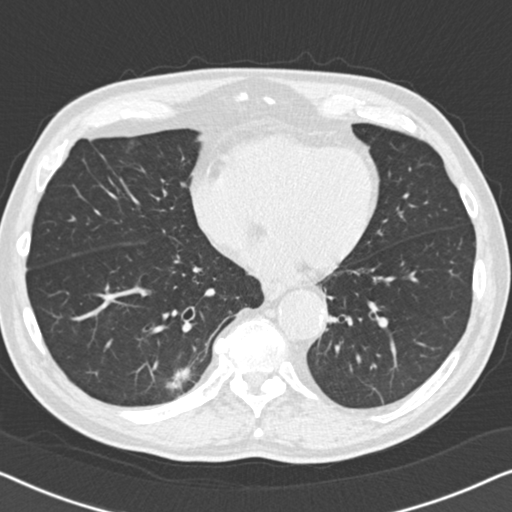
Axial slice from a low-dose chest CT screening exam; second screening round (one year after baseline); lung window (W 1500 / L -600 HU); 2 mm slice thickness; standard (soft-tissue) reconstruction kernel (B30f); slice 114 of 164 in the series; 512 × 512 image matrix. Male participant, aged 74 years at enrolment. Current smoker at enrolment.
- Expert reader's lesion annotation, bounding box [x1, y1, x2, y2] px = [150, 347, 219, 406].
- The screening reader recorded 5 non-calcified nodules or masses ≥4 mm on this exam; which of them this box marks is not recorded.
- Official screen result: positive, other.
- Lung cancer was diagnosed 55 days after this screen: bronchiolo-alveolar adenocarcinoma, NOS, right lower lobe, moderately differentiated (G2), stage IA (AJCC 6th edition), 16 mm at pathology.